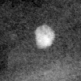
Crop from a digitized film mammogram around one marked abnormality; right breast; CC view.
Calcifications, morphology round and regular / lucent center; BI-RADS assessment category 2; subtlety rating 4 on a 1 (subtle) to 5 (obvious) scale; benign; no additional work-up was recommended (benign without callback).